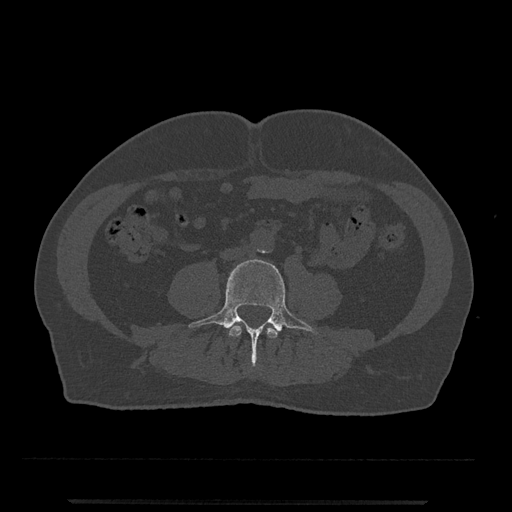
CT including the spine, one axial slice. Position 148 of 797 along the scan axis. Reconstruction kernel Br40s/3. 120 kVp. Bone window (W 1800 / L 400 HU). 0.5 mm slice thickness. 512 × 512 image matrix, field of view 419 × 419 mm. Male patient, age 63 years. Case-level facts recorded for this patient, not image findings: primary cancer: prostate.
Outlined on this slice (semi-automatically segmented with operator editing):
- L3 vertebra: box from (x=228, y=324) to (x=278, y=339) px
- L4 vertebra: (x=189, y=259)–(x=318, y=366)